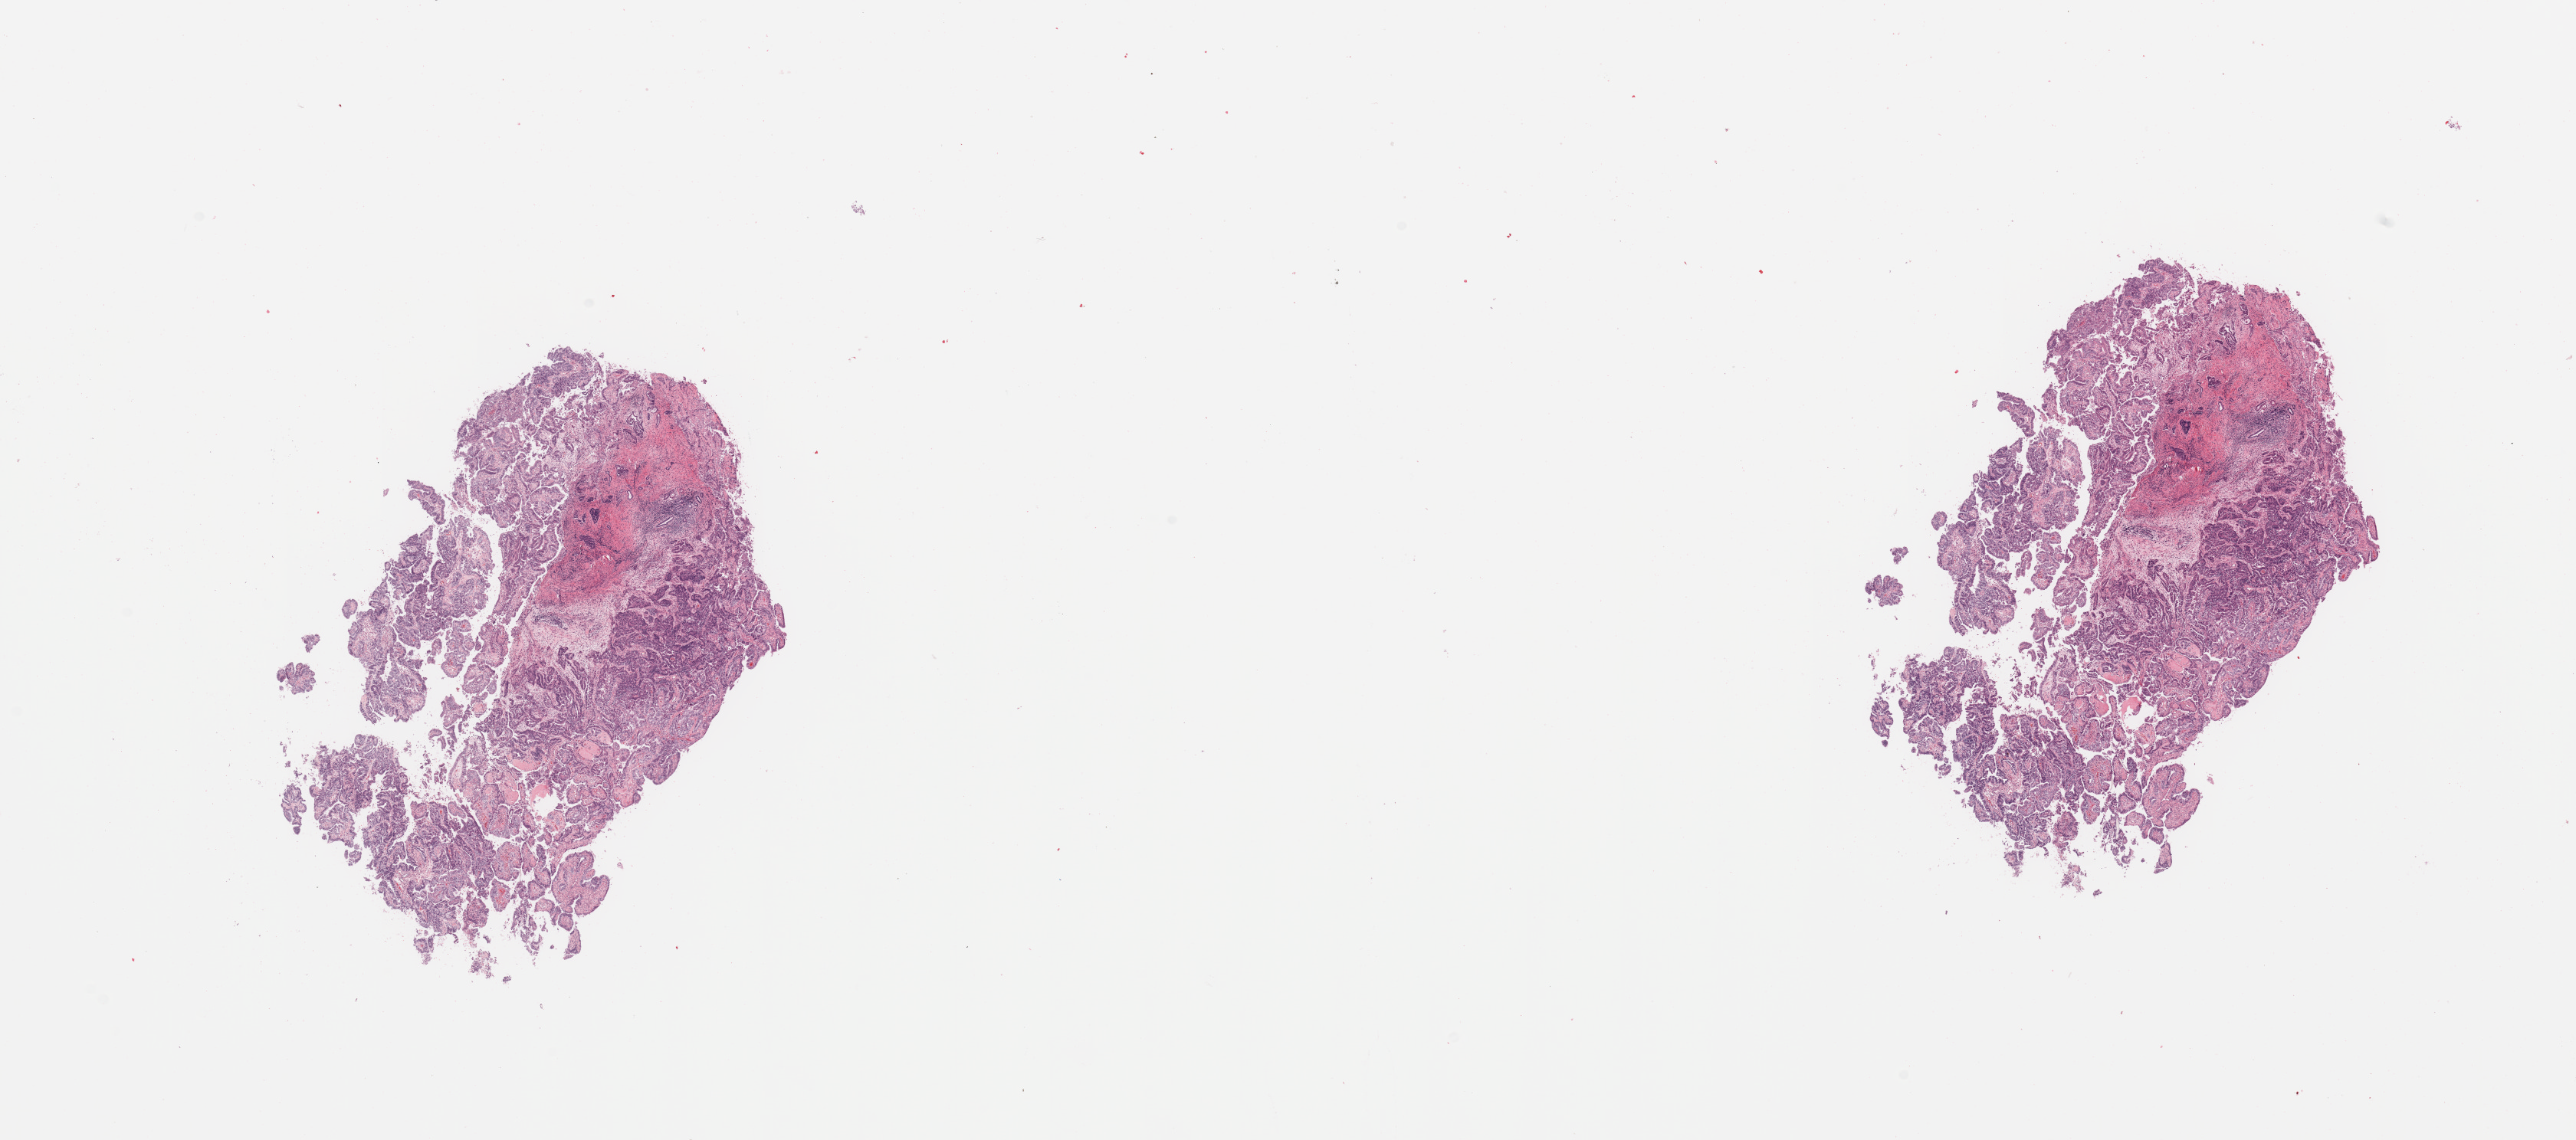
Digitized Hematoxylin and eosin (H&E) stained tissue section (whole slide) — low-resolution overview of the scanned area, about 26.6 x 11.8 mm, uterus, tumour tissue. Female, 86 y/o. Histologic grade: G2 (moderately differentiated).
AJCC pathologic stage: IB. Diagnosis: Endometrioid adenocarcinoma, NOS.